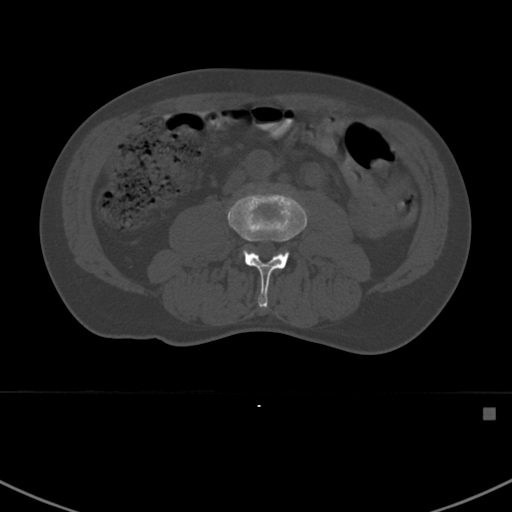
CT including the spine, one axial slice; position 259 of 412 along the scan axis; bone window (W 1800 / L 400 HU); 512 × 512 image matrix, field of view 358 × 358 mm. Male patient, age 59 years. Case-level facts recorded for this patient, not image findings: primary cancer: prostate.
Structures marked on this image (semi-automatically segmented with operator editing):
- L3 vertebra: box from (x=228, y=192) to (x=307, y=309) px
- L4 vertebra: (x=242, y=249)–(x=247, y=254)